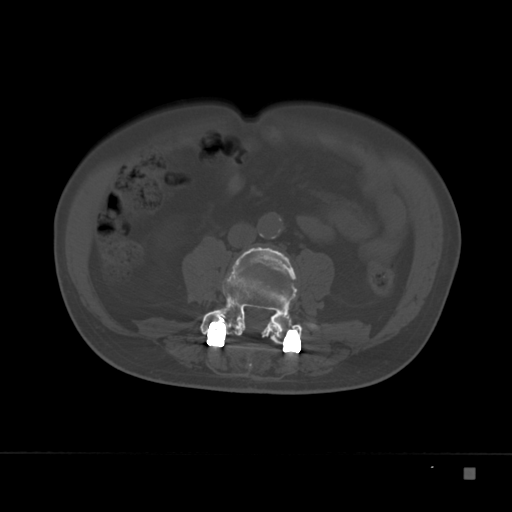
CT including the spine, one axial slice. Position 53 of 332 along the scan axis. Reconstruction kernel Br40s. 120 kVp. Bone window (W 1800 / L 400 HU). 1.5 mm slice thickness. 512 × 512 image matrix, field of view 389 × 389 mm. Male patient, age 72 years. From the clinical record (not read from this slice): primary cancer: skeletal.
Structures marked on this image (semi-automatically segmented with operator editing):
- L3 vertebra: bounding box [x1, y1, x2, y2] px = [235, 247, 297, 328]
- L4 vertebra: [200, 261, 317, 344]